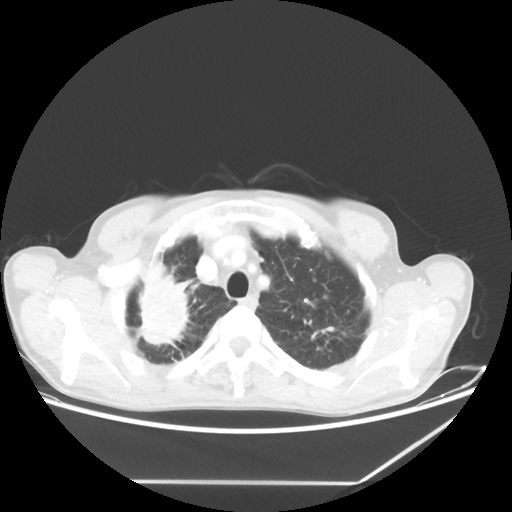
Chest CT, one axial slice; slice 54 of 65 in the series (ordered by position); reconstruction kernel STANDARD; 80 kVp; lung window (W 1500 / L -600 HU); 512 × 512 image matrix, field of view 397 × 397 mm. Patient: male, 68 years. Case-level facts recorded for this patient, not image findings: clinical TNM (as recorded): T3 N3 M0.
Annotated regions visible in this slice (rectangle marked by the reading radiologist):
- lung tumour (recorded histology: adenocarcinoma): bounding box [x1, y1, x2, y2] px = [128, 254, 204, 361]